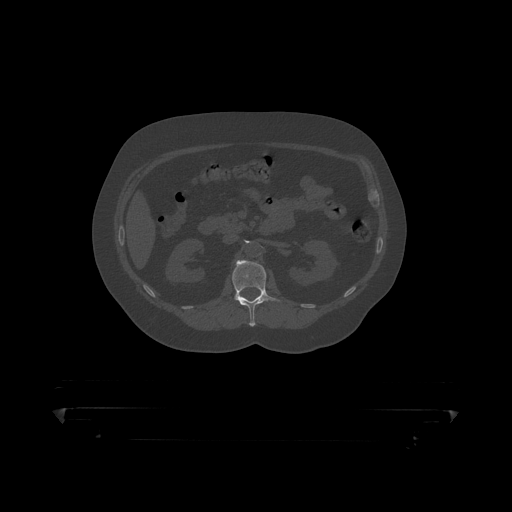
CT including the spine, one axial slice. Position 142 of 390 along the scan axis. 120 kVp. Bone window (W 1800 / L 400 HU). 512 × 512 image matrix, field of view 650 × 650 mm. Patient: male, 60 years. Case-level facts recorded for this patient, not image findings: primary cancer: prostate.
Outlined on this slice (semi-automatically segmented with operator editing):
- L1 vertebra: bounding box <232,261,282,319> (left, top, right, bottom; pixels)